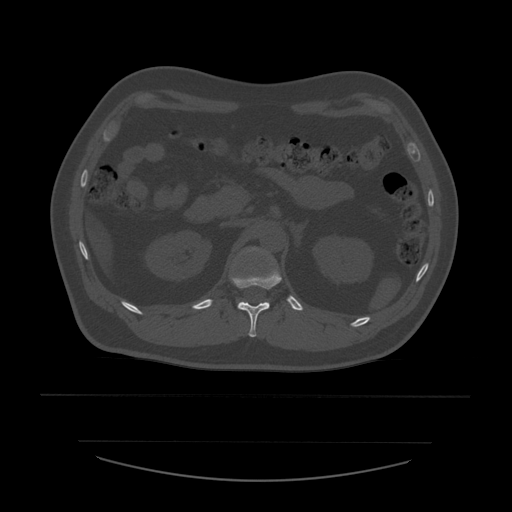
CT including the spine, one axial slice; slice 244 of 532 in the series (ordered by position); reconstruction kernel STANDARD; 120 kVp; bone window (W 1800 / L 400 HU); 1.25 mm slice thickness; 512 × 512 image matrix, field of view 441 × 441 mm. Patient age 44 years. From the clinical record (not read from this slice): primary cancer: soft tissue sarcoma.
Structures marked on this image (semi-automatically segmented with operator editing):
- L1 vertebra: bounding box (x1, y1, x2, y2) in pixels: (239, 251, 262, 304)
- T12 vertebra: (231, 264, 282, 337)